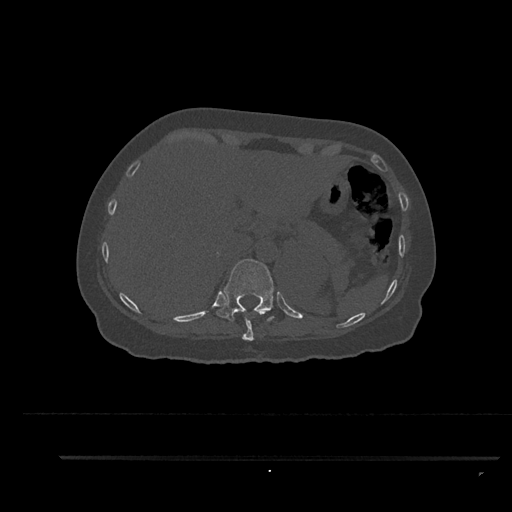
CT including the spine, one axial slice. Slice 331 of 797 in the series (ordered by position). Bone window (W 1800 / L 400 HU). 512 × 512 image matrix. Patient: female, 44 years. Case-level facts recorded for this patient, not image findings: primary cancer: renal; vertebrae with lytic lesions (as recorded): L1.
Structures marked on this image (semi-automatically segmented with operator editing):
- T10 vertebra: bounding box (x1, y1, x2, y2) in pixels: (242, 308, 254, 341)
- T11 vertebra: (216, 259, 275, 322)